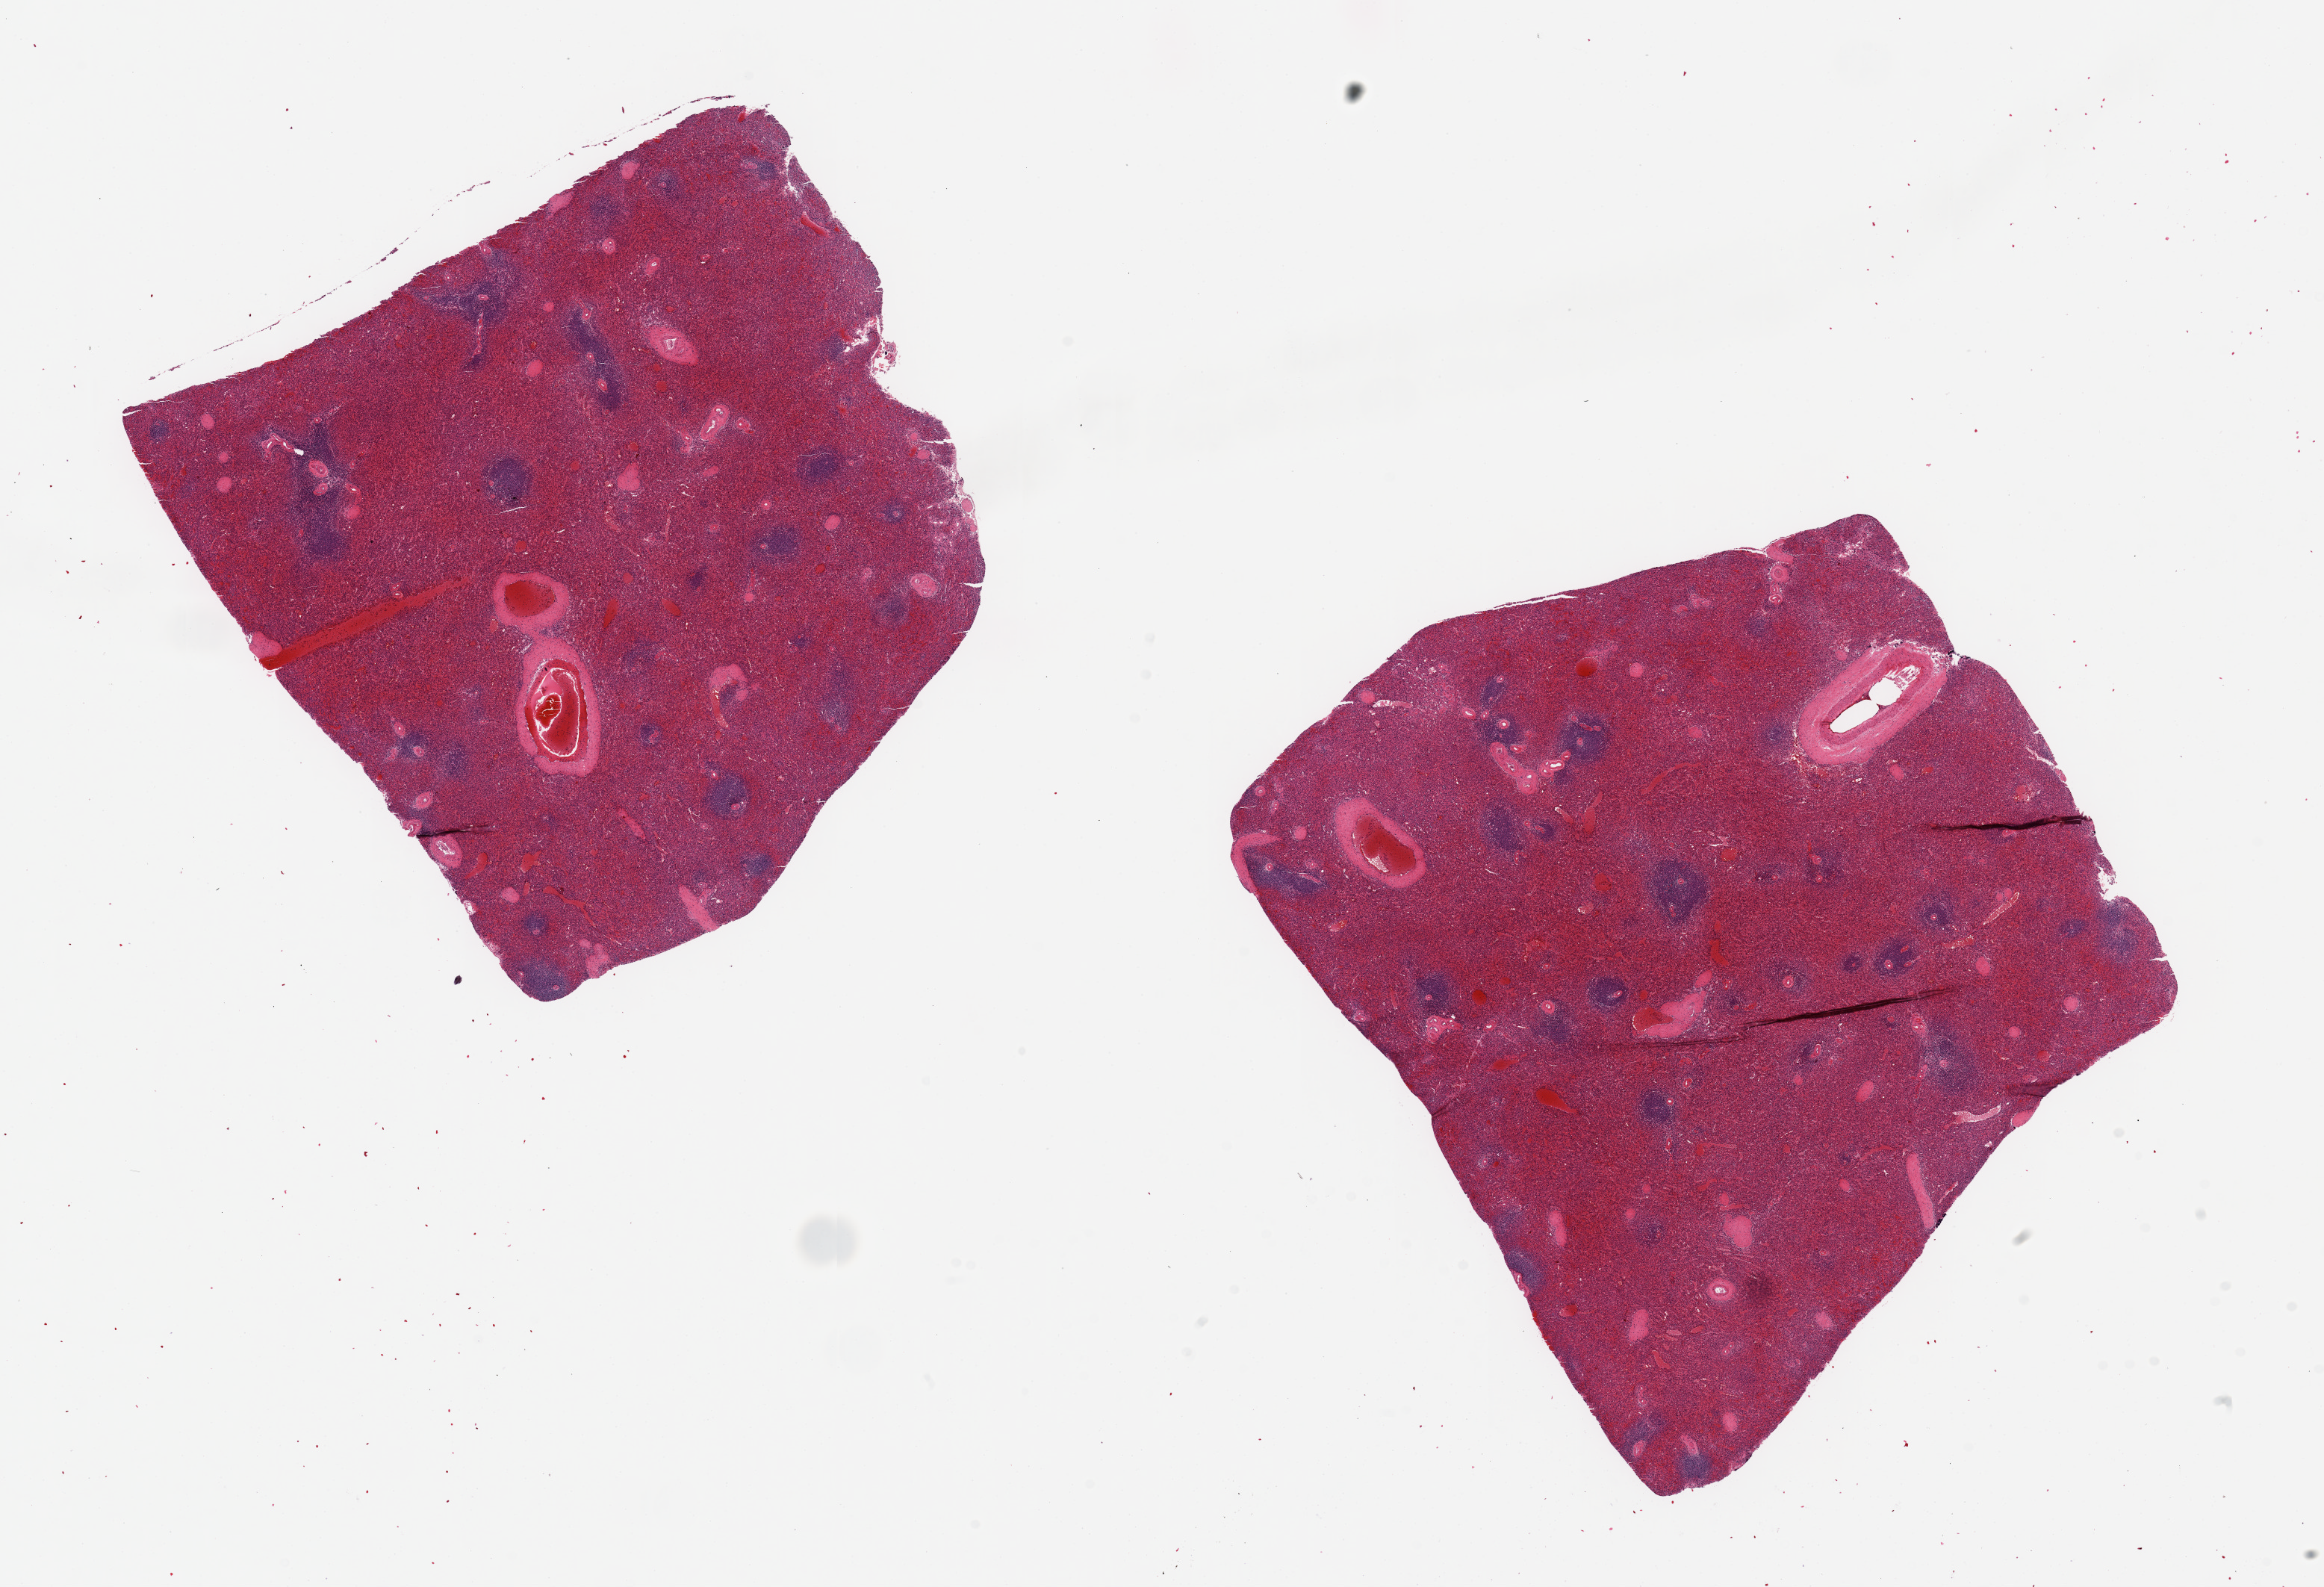
Digitized hematoxylin and eosin (H&E)-stained section, shown as a low-resolution overview of the whole scanned area (about 24.6 x 16.8 mm). PAXgene-fixed, paraffin-embedded tissue. Target tissue: spleen. Tissue donor sample. Donor sex: female.
Pathologist's review note for this sample: 2 pieces, 8x8 & 9x8mm; well preserved.